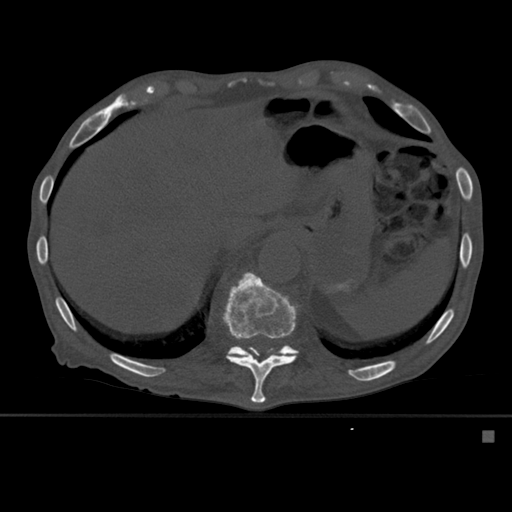
CT including the spine, one axial slice. Bone window (W 1800 / L 400 HU). 1.5 mm slice thickness. 512 × 512 image matrix. Male patient, age 78 years. From the clinical record (not read from this slice): primary cancer: prostate.
Outlined on this slice (semi-automatic segmentation, software-assisted and operator-edited):
- T11 vertebra: box from (x=222, y=272) to (x=298, y=404) px
- T12 vertebra: (x=226, y=345)–(x=299, y=359)